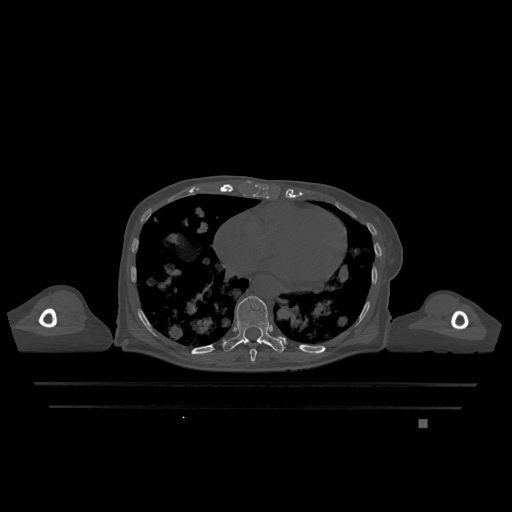
CT including the spine, one axial slice; position 656 of 1317 along the scan axis; bone window (W 1800 / L 400 HU); 0.5 mm slice thickness; 512 × 512 image matrix. Female patient, age 74 years. From the clinical record (not read from this slice): primary cancer: lung; vertebrae with lytic lesions (as recorded): T1, T4, T5, T6, L4, L5.
Annotated regions visible in this slice (semi-automatic segmentation, software-assisted and operator-edited):
- T10 vertebra: box from (x=222, y=296) to (x=284, y=353) px
- T9 vertebra: (x=250, y=348)–(x=257, y=362)